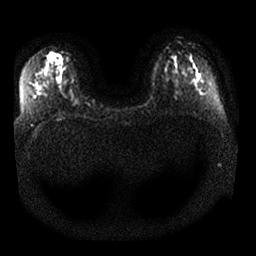
Breast MRI, one axial slice; position 14 of 25 along the scan axis; diffusion-weighted series; image 2 of 4 stored at this slice position (different b-values; order by instance number); 1.5 T; 4 mm slice thickness; 256 × 256 image matrix. Female patient.
Annotated regions visible in this slice (expert manual segmentation):
- tumour on diffusion-weighted imaging: bounding box <46,52,62,65> (left, top, right, bottom; pixels)